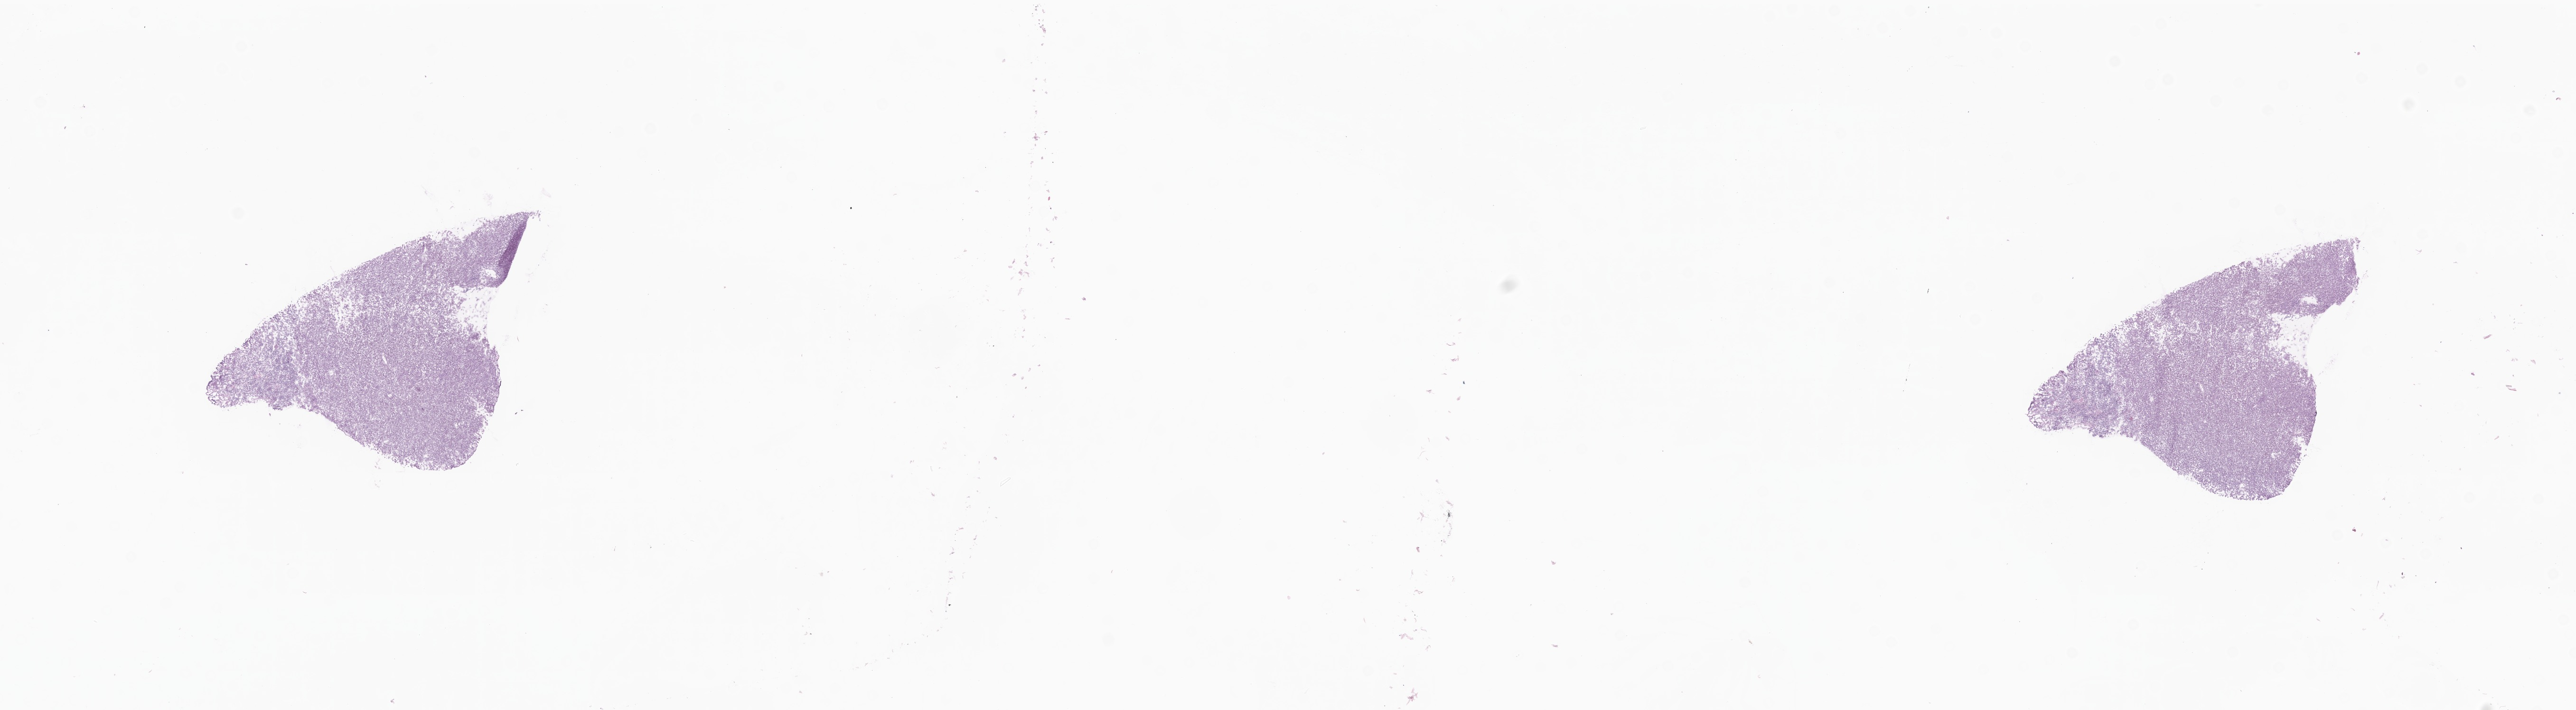
Digitized haematoxylin and eosin-stained section — whole scanned area (about 22.9 x 6.3 mm) shown as a low-resolution overview, cryosection, specimen: metastatic tumor tissue, resected from lymph nodes of axilla or arm. Male patient; age at initial diagnosis 78 years. Composition of this section per pathologist review: tumor cells 100%, tumor nuclei 98%.
Patient diagnosis (primary): Malignant melanoma, NOS.